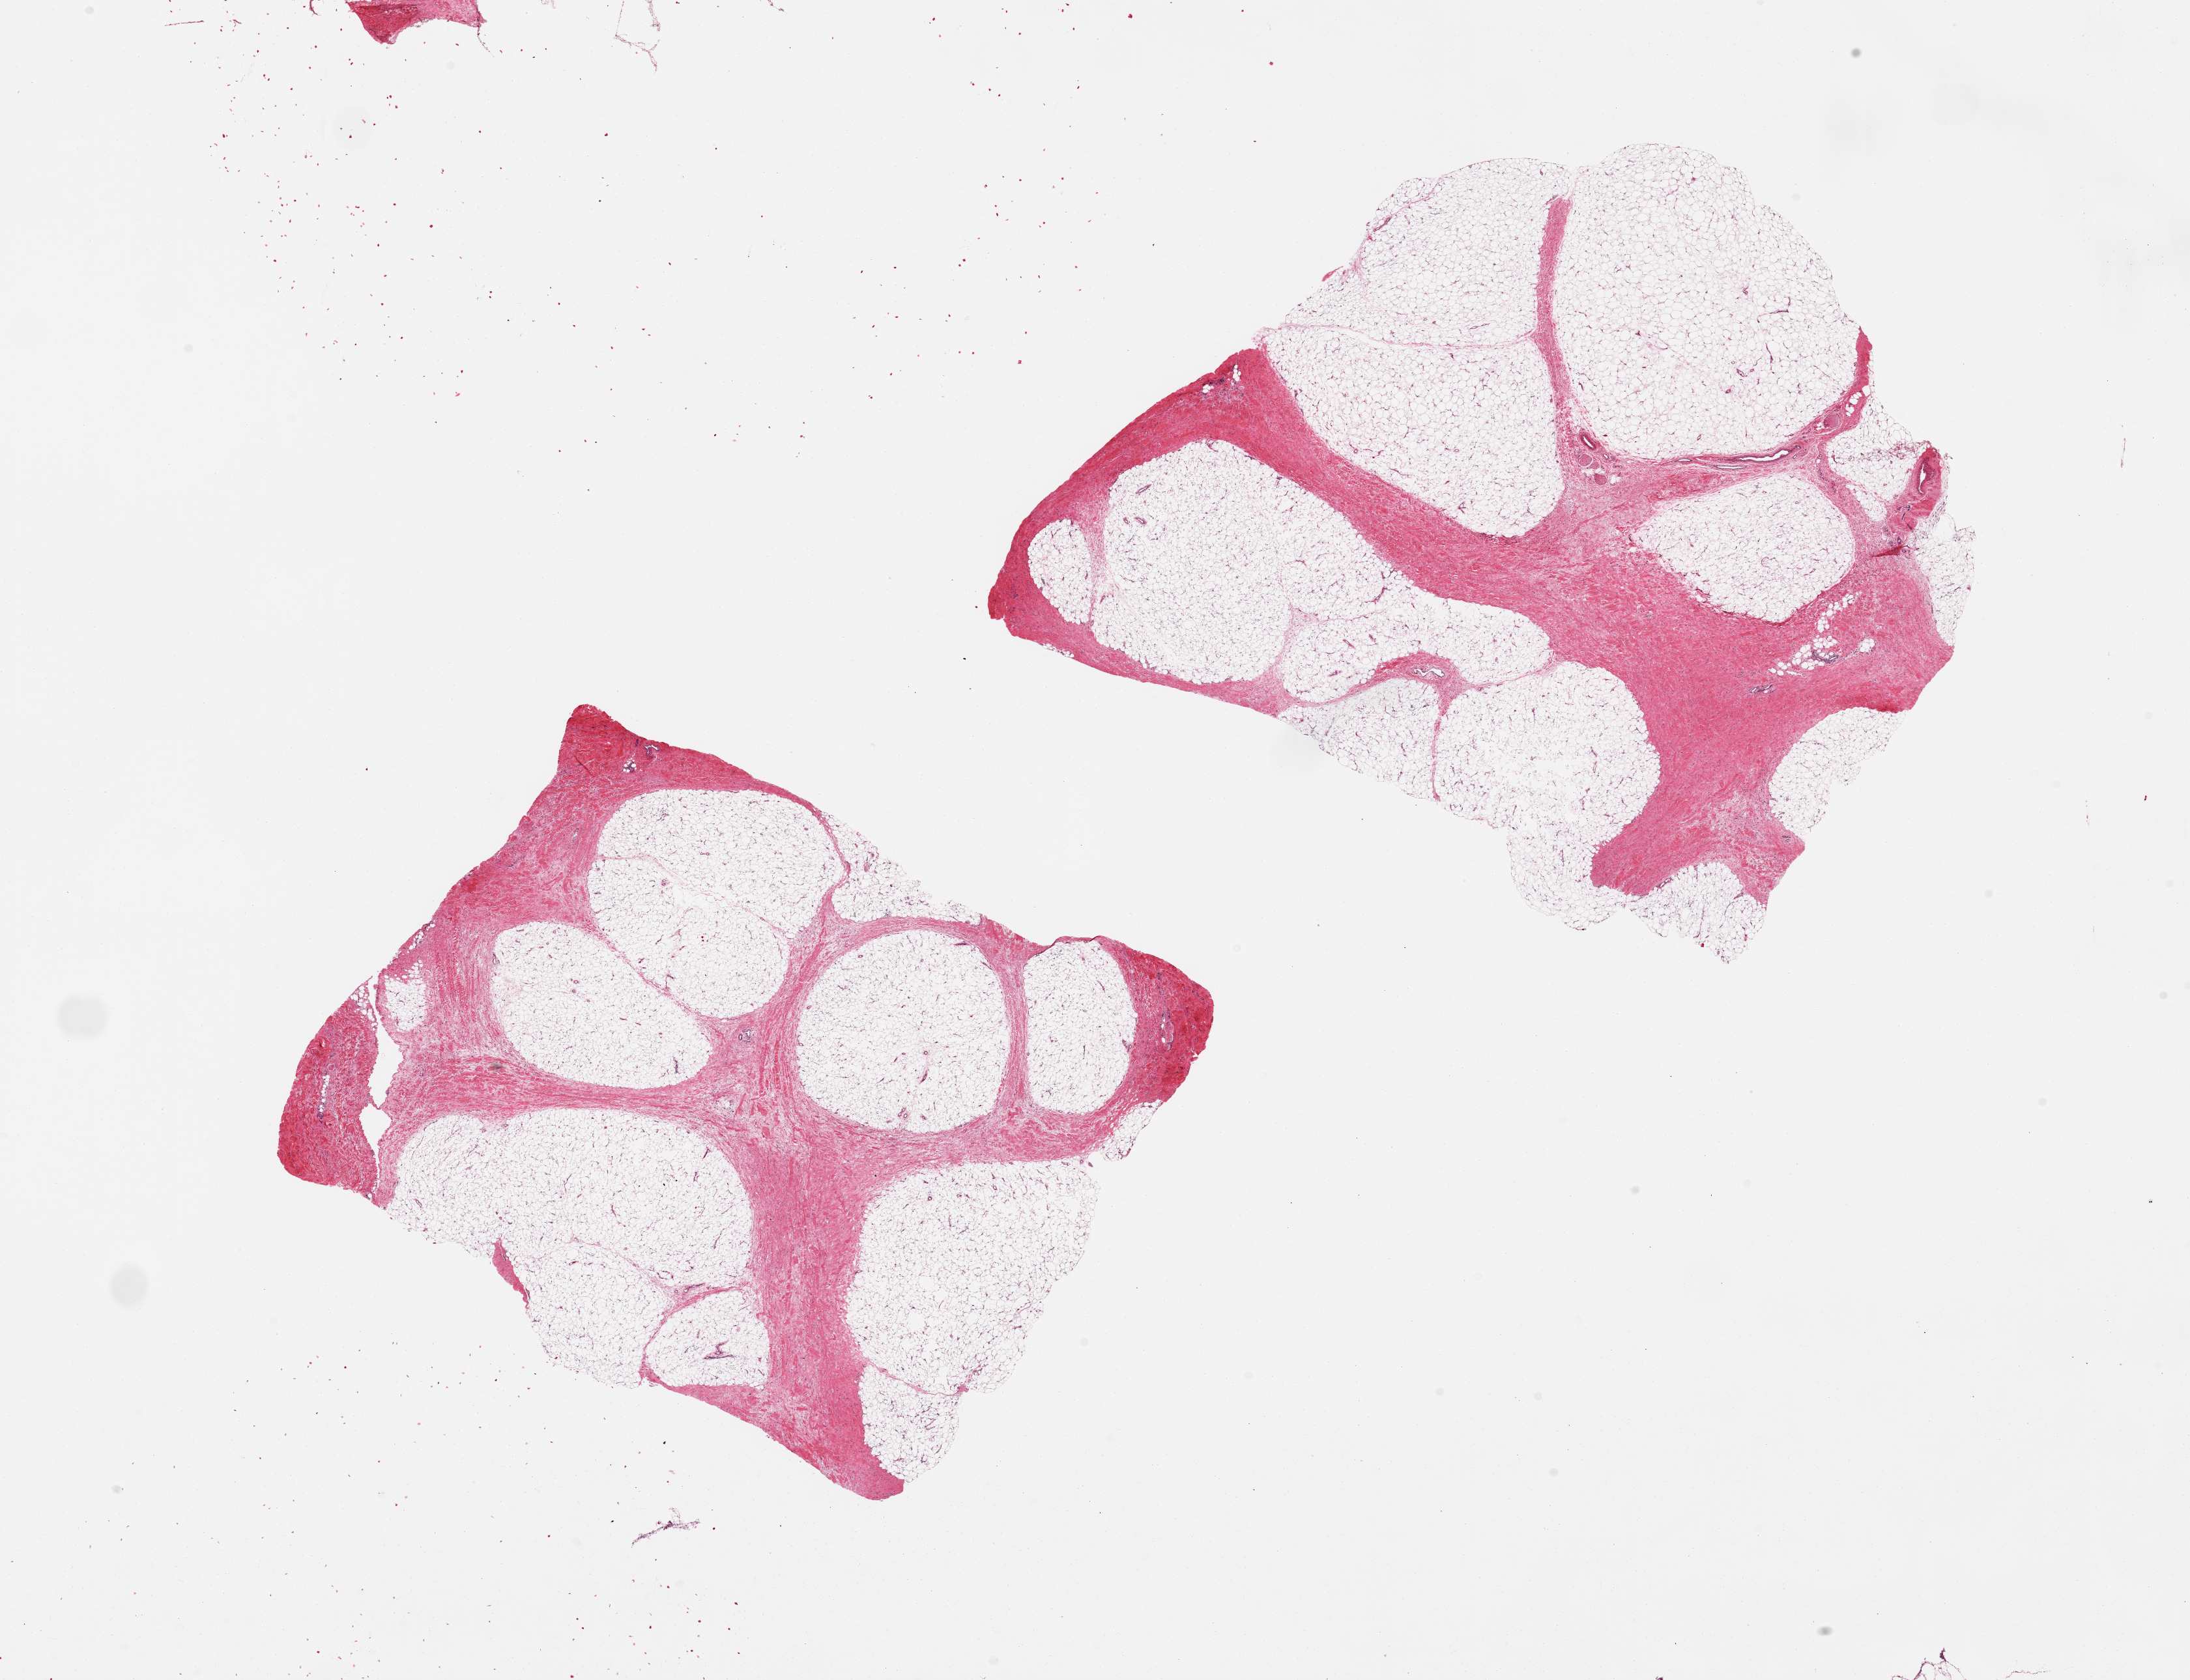
Whole-slide image, hematoxylin and eosin (H&E) stain, whole scanned area (about 26.6 x 20.4 mm) shown as a low-resolution overview, PAXgene-fixed, paraffin-embedded tissue, target tissue: adipose tissue, donor tissue sample. Donor: male.
• pathologist's review note for this sample: 2 pieces, 9x8 & 10x10mm; dense pink fidbrosu tissue is ~50% of both sections